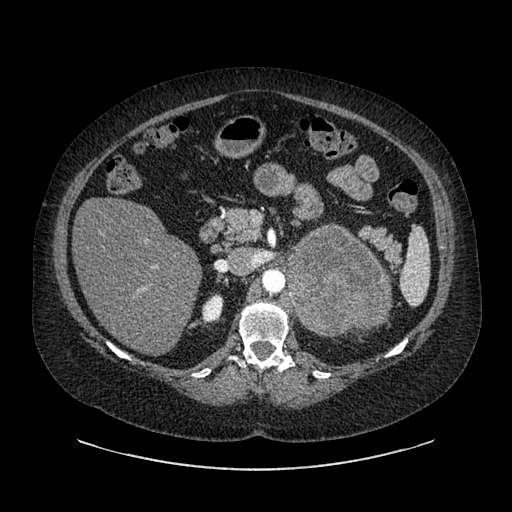
Contrast-enhanced abdominal CT, one axial slice; position 553 of 769 along the scan axis; 120 kVp; intravenous contrast given; soft-tissue window (W 400 / L 40 HU); 0.62 mm slice thickness; 512 × 512 image matrix. Patient: female, 61 years. From the clinical record (not read from this slice): diagnosis: adrenocortical carcinoma; tumour side: left adrenal; tumour size at pathology: 13 cm; Ki-67 index: 79 %; stage (as recorded): 2.
Structures marked on this image (semi-automatically segmented with operator editing):
- mass: bounding box <289,228,387,335> (left, top, right, bottom; pixels)